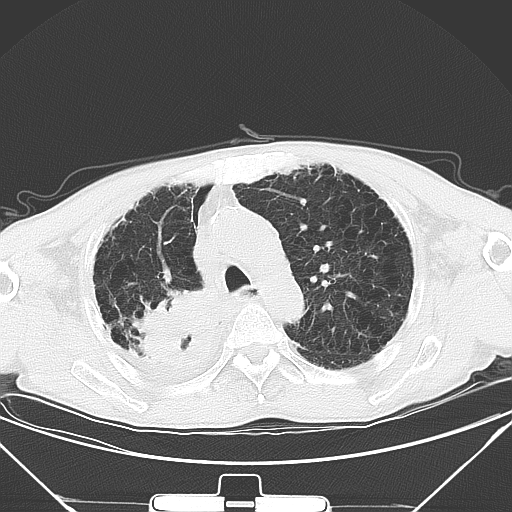
Chest CT, one axial slice. Slice 35 of 50 in the series (ordered by position). Lung window (W 1500 / L -600 HU). 5 mm slice thickness. 512 × 512 image matrix, field of view 373 × 373 mm. Male patient, age 65 years. Case-level facts recorded for this patient, not image findings: clinical TNM (as recorded): T3 N1 M1a.
Structures marked on this image (bounding box drawn by a radiologist):
- lung tumour (recorded histology: squamous cell carcinoma): bounding box (x1, y1, x2, y2) in pixels: (138, 289, 227, 377)